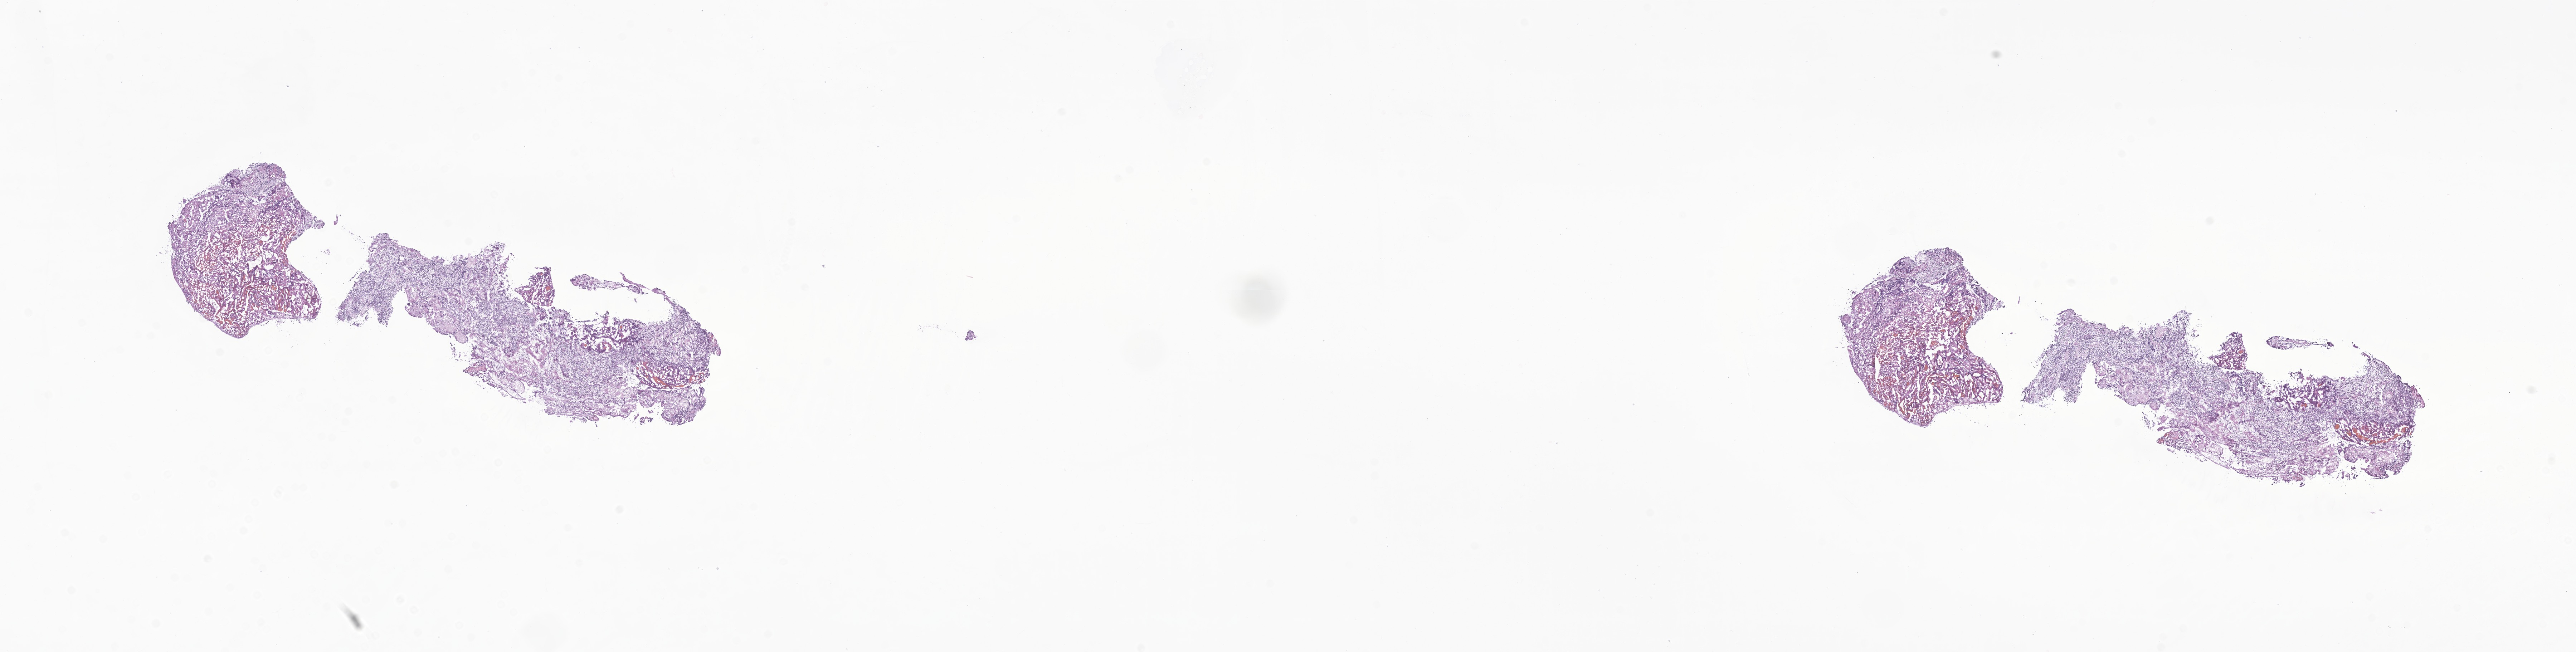
Hematoxylin and eosin (H&E) whole-slide image of tumor tissue from the brain, low-resolution overview of the scanned area, about 30.3 x 7.7 mm, frozen section (OCT-embedded). Patient male; age 882 days (about 2.4 years).
Recorded diagnosis: Medulloblastoma, NOS.